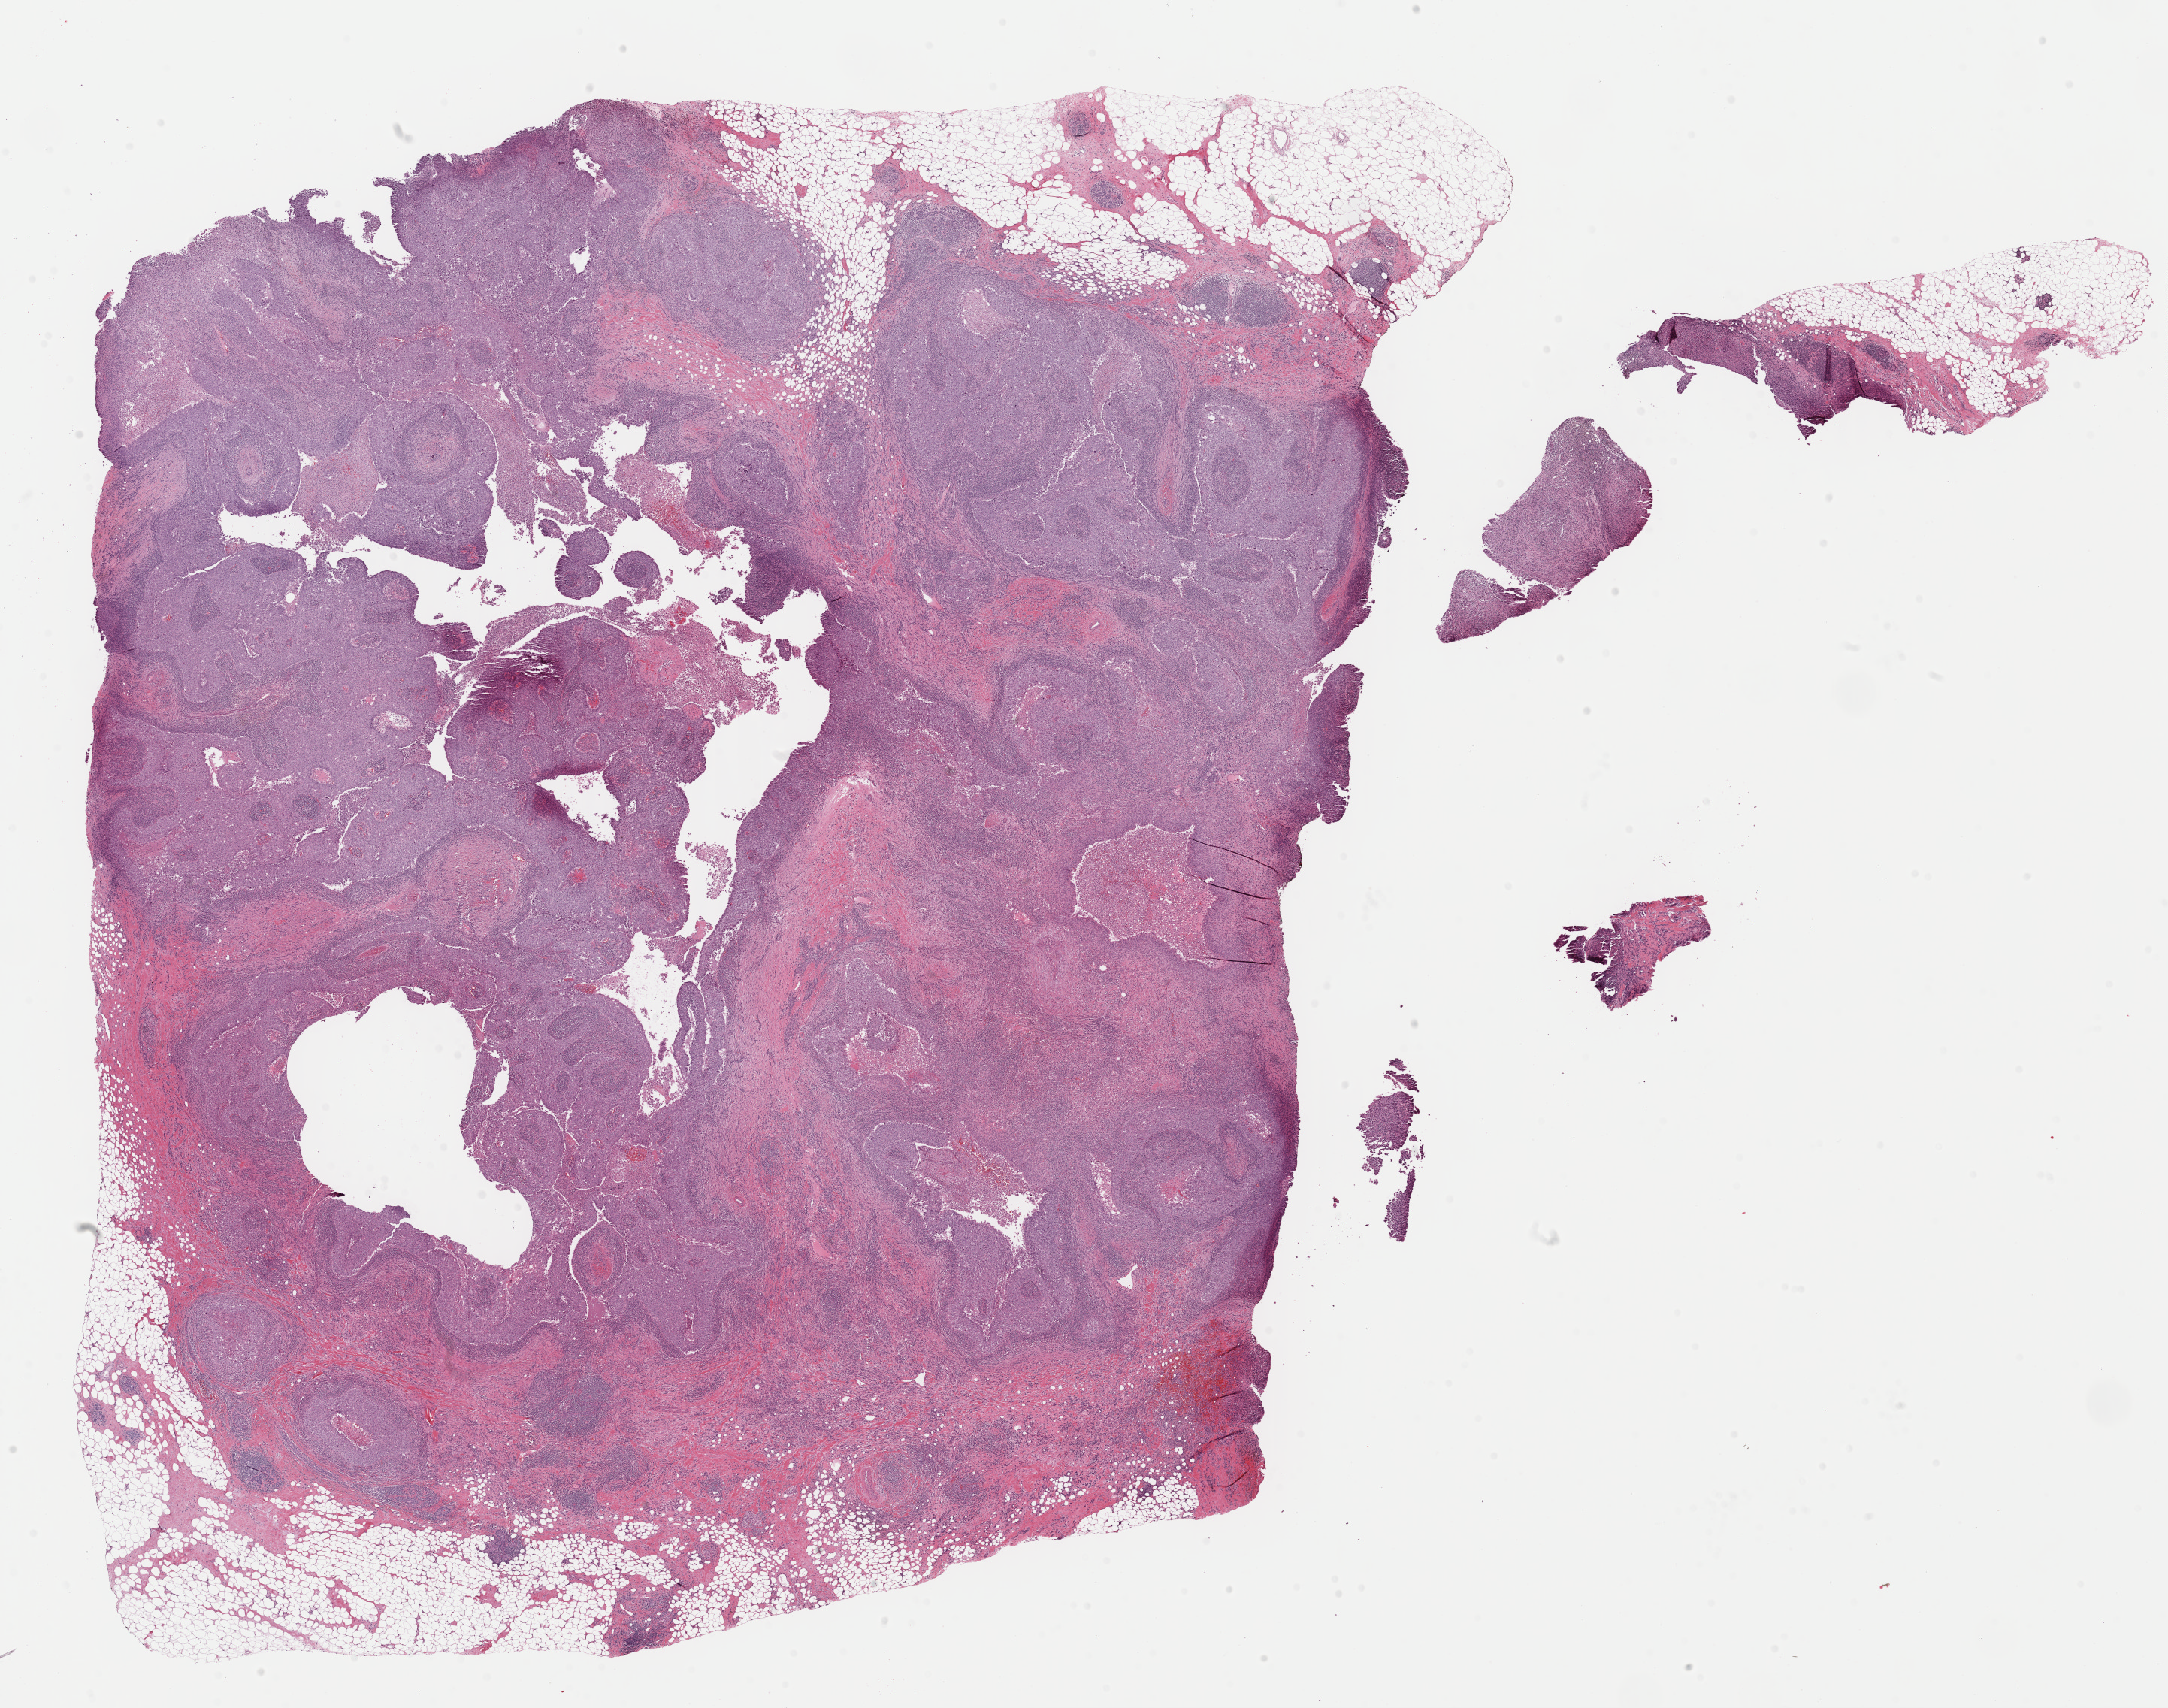
H&E-stained whole-slide image, a low-resolution overview of the entire scanned area, about 22.8 x 18.0 mm (slide scanned at 40x). Formalin-fixed paraffin-embedded (FFPE) diagnostic section. Sample: primary tumour, breast. Female, age 47 years at initial diagnosis.
* AJCC pathologic stage: IIA (6th edition)
* laterality: left
* histologic diagnosis: Medullary carcinoma, NOS
* lymph nodes positive (case pathology): 0 of 5 examined